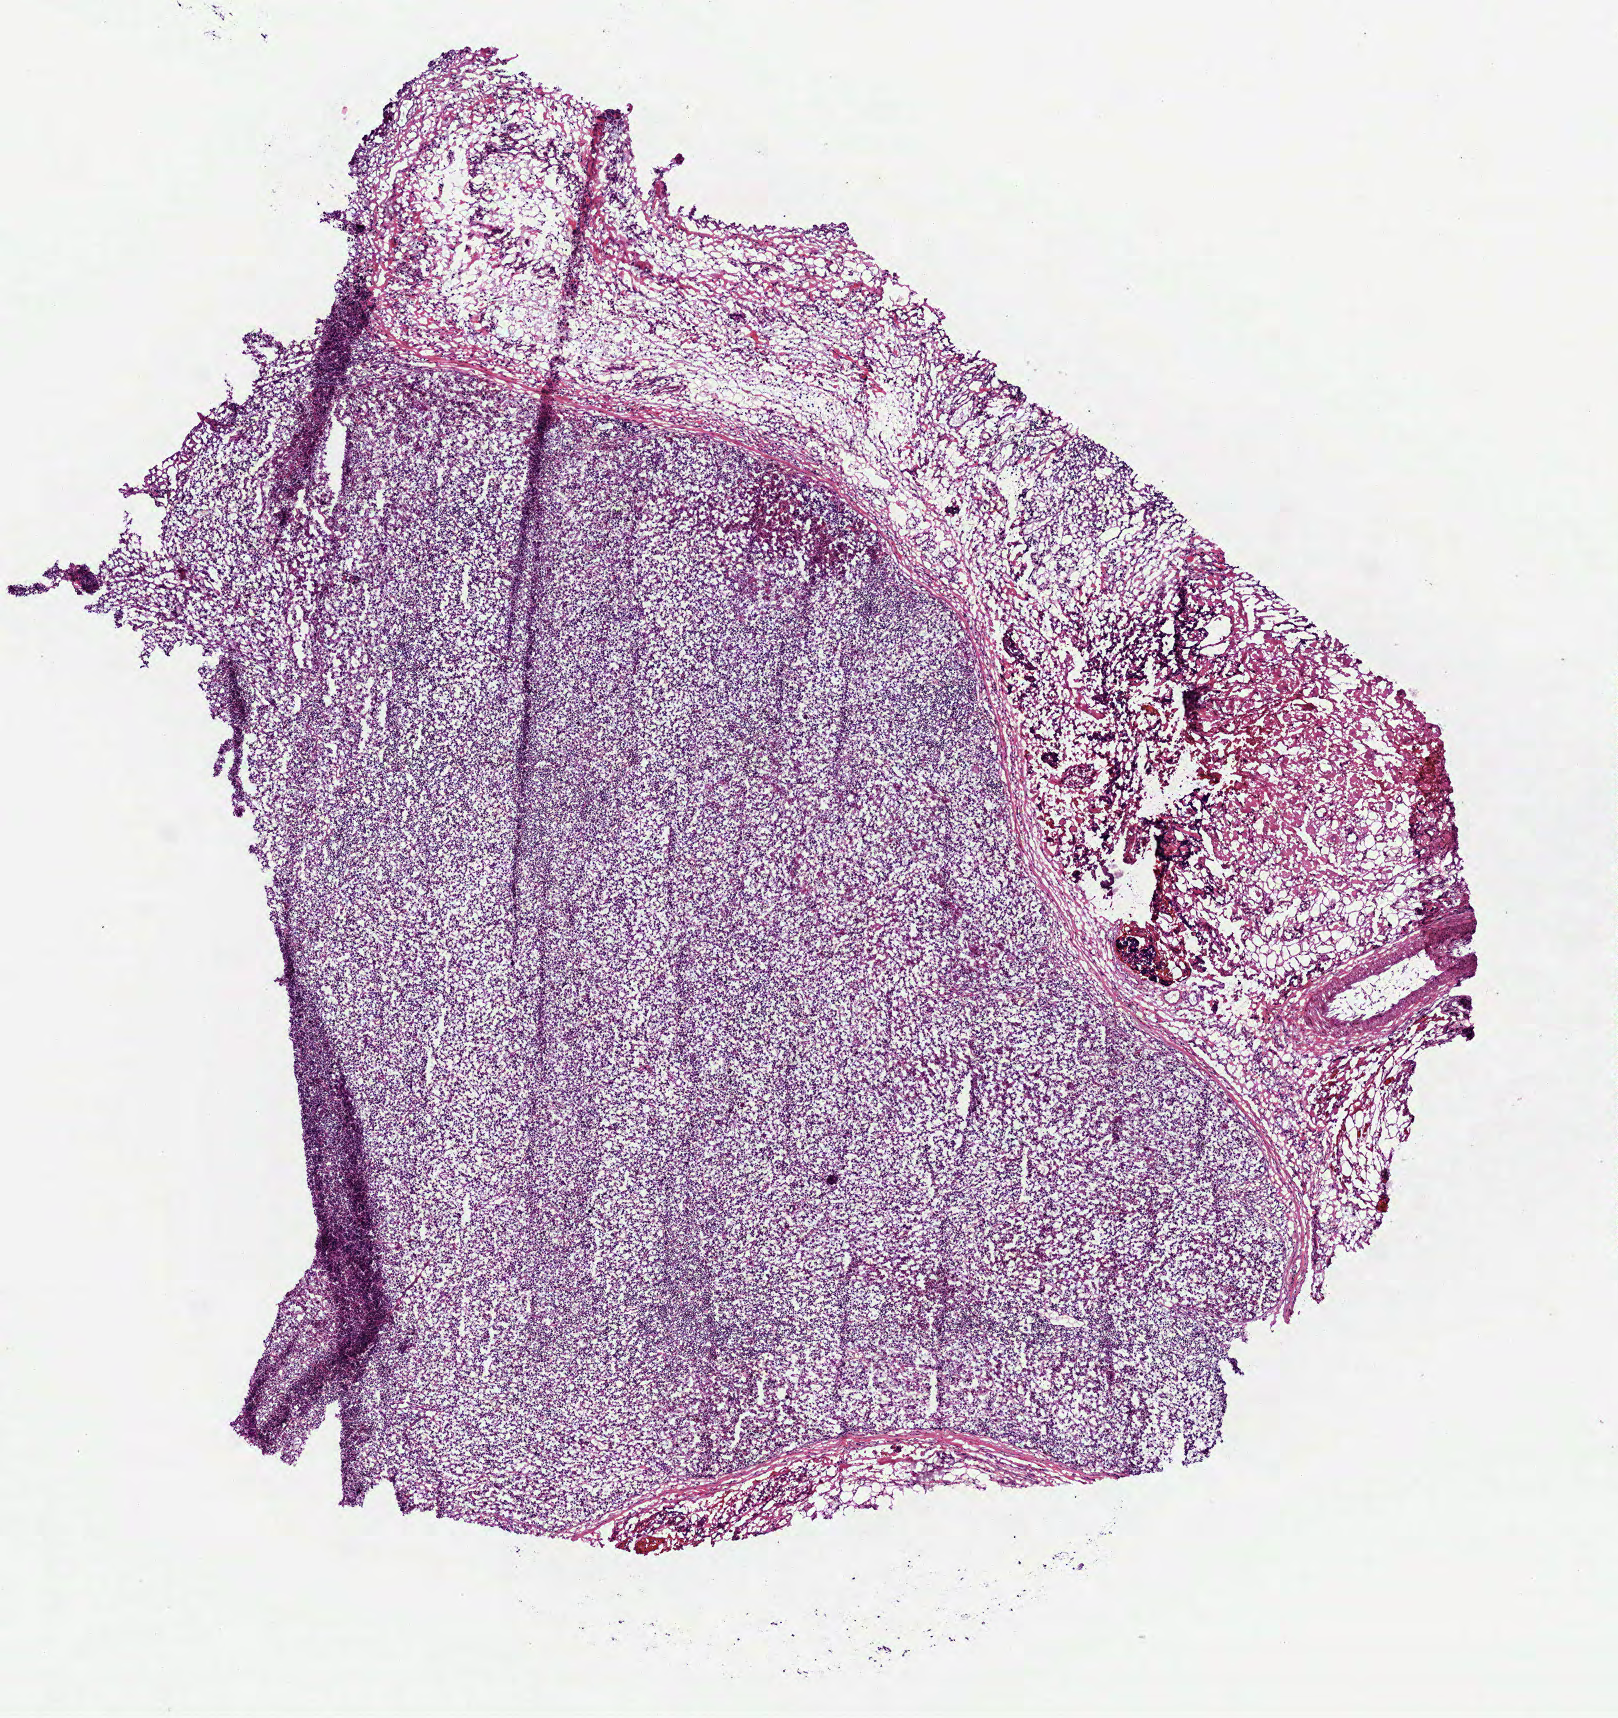
Whole-slide histology image, H&E — a low-resolution overview of the entire scanned area, about 6.5 x 6.9 mm (from a 40x scan). Frozen section from the top of the tissue portion. Primary tumour sample from the lymphoid tissue. Male, age 51 years at initial diagnosis. Pathologist review of this section (percent, as recorded): tumour cells 70%, tumour nuclei 80%, normal cells 0%, stromal cells 25%, necrosis 5%. Infiltration values recorded for this section: lymphocyte infiltration 10%, monocyte infiltration 0%, neutrophil infiltration 0%.
* histologic diagnosis: Diffuse large B-cell lymphoma, NOS (submandibular gland)